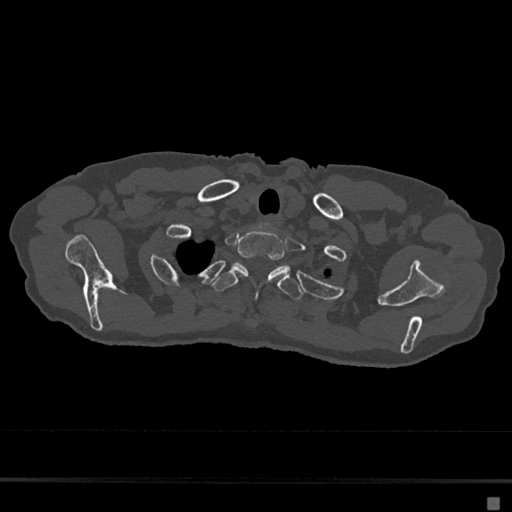
CT including the spine, one axial slice; slice 593 of 797 in the series (ordered by position); 120 kVp; bone window (W 1800 / L 400 HU); 512 × 512 image matrix. Patient: female, 68 years. Case-level facts recorded for this patient, not image findings: primary cancer: renal.
Structures marked on this image (semi-automatic segmentation, software-assisted and operator-edited):
- T1 vertebra: box from (x=236, y=230) to (x=290, y=271) px
- T2 vertebra: (x=212, y=262)–(x=304, y=302)